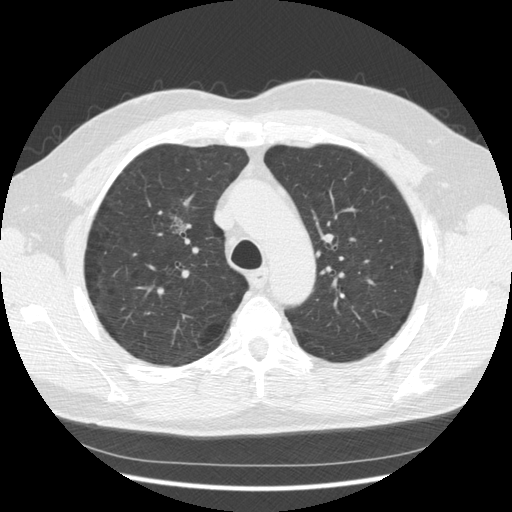
Low-dose screening chest CT, one axial slice. Position 91 of 133 along the scan axis. 140 kVp. Lung window (W 1500 / L -600 HU). 2.5 mm slice thickness. 512 × 512 image matrix, field of view 369 × 369 mm.
Structures marked on this image (outlined manually by an expert reader):
- lesion 1 (tumor, upper lobe of right lung): bounding box [x1, y1, x2, y2] px = [174, 217, 186, 233]